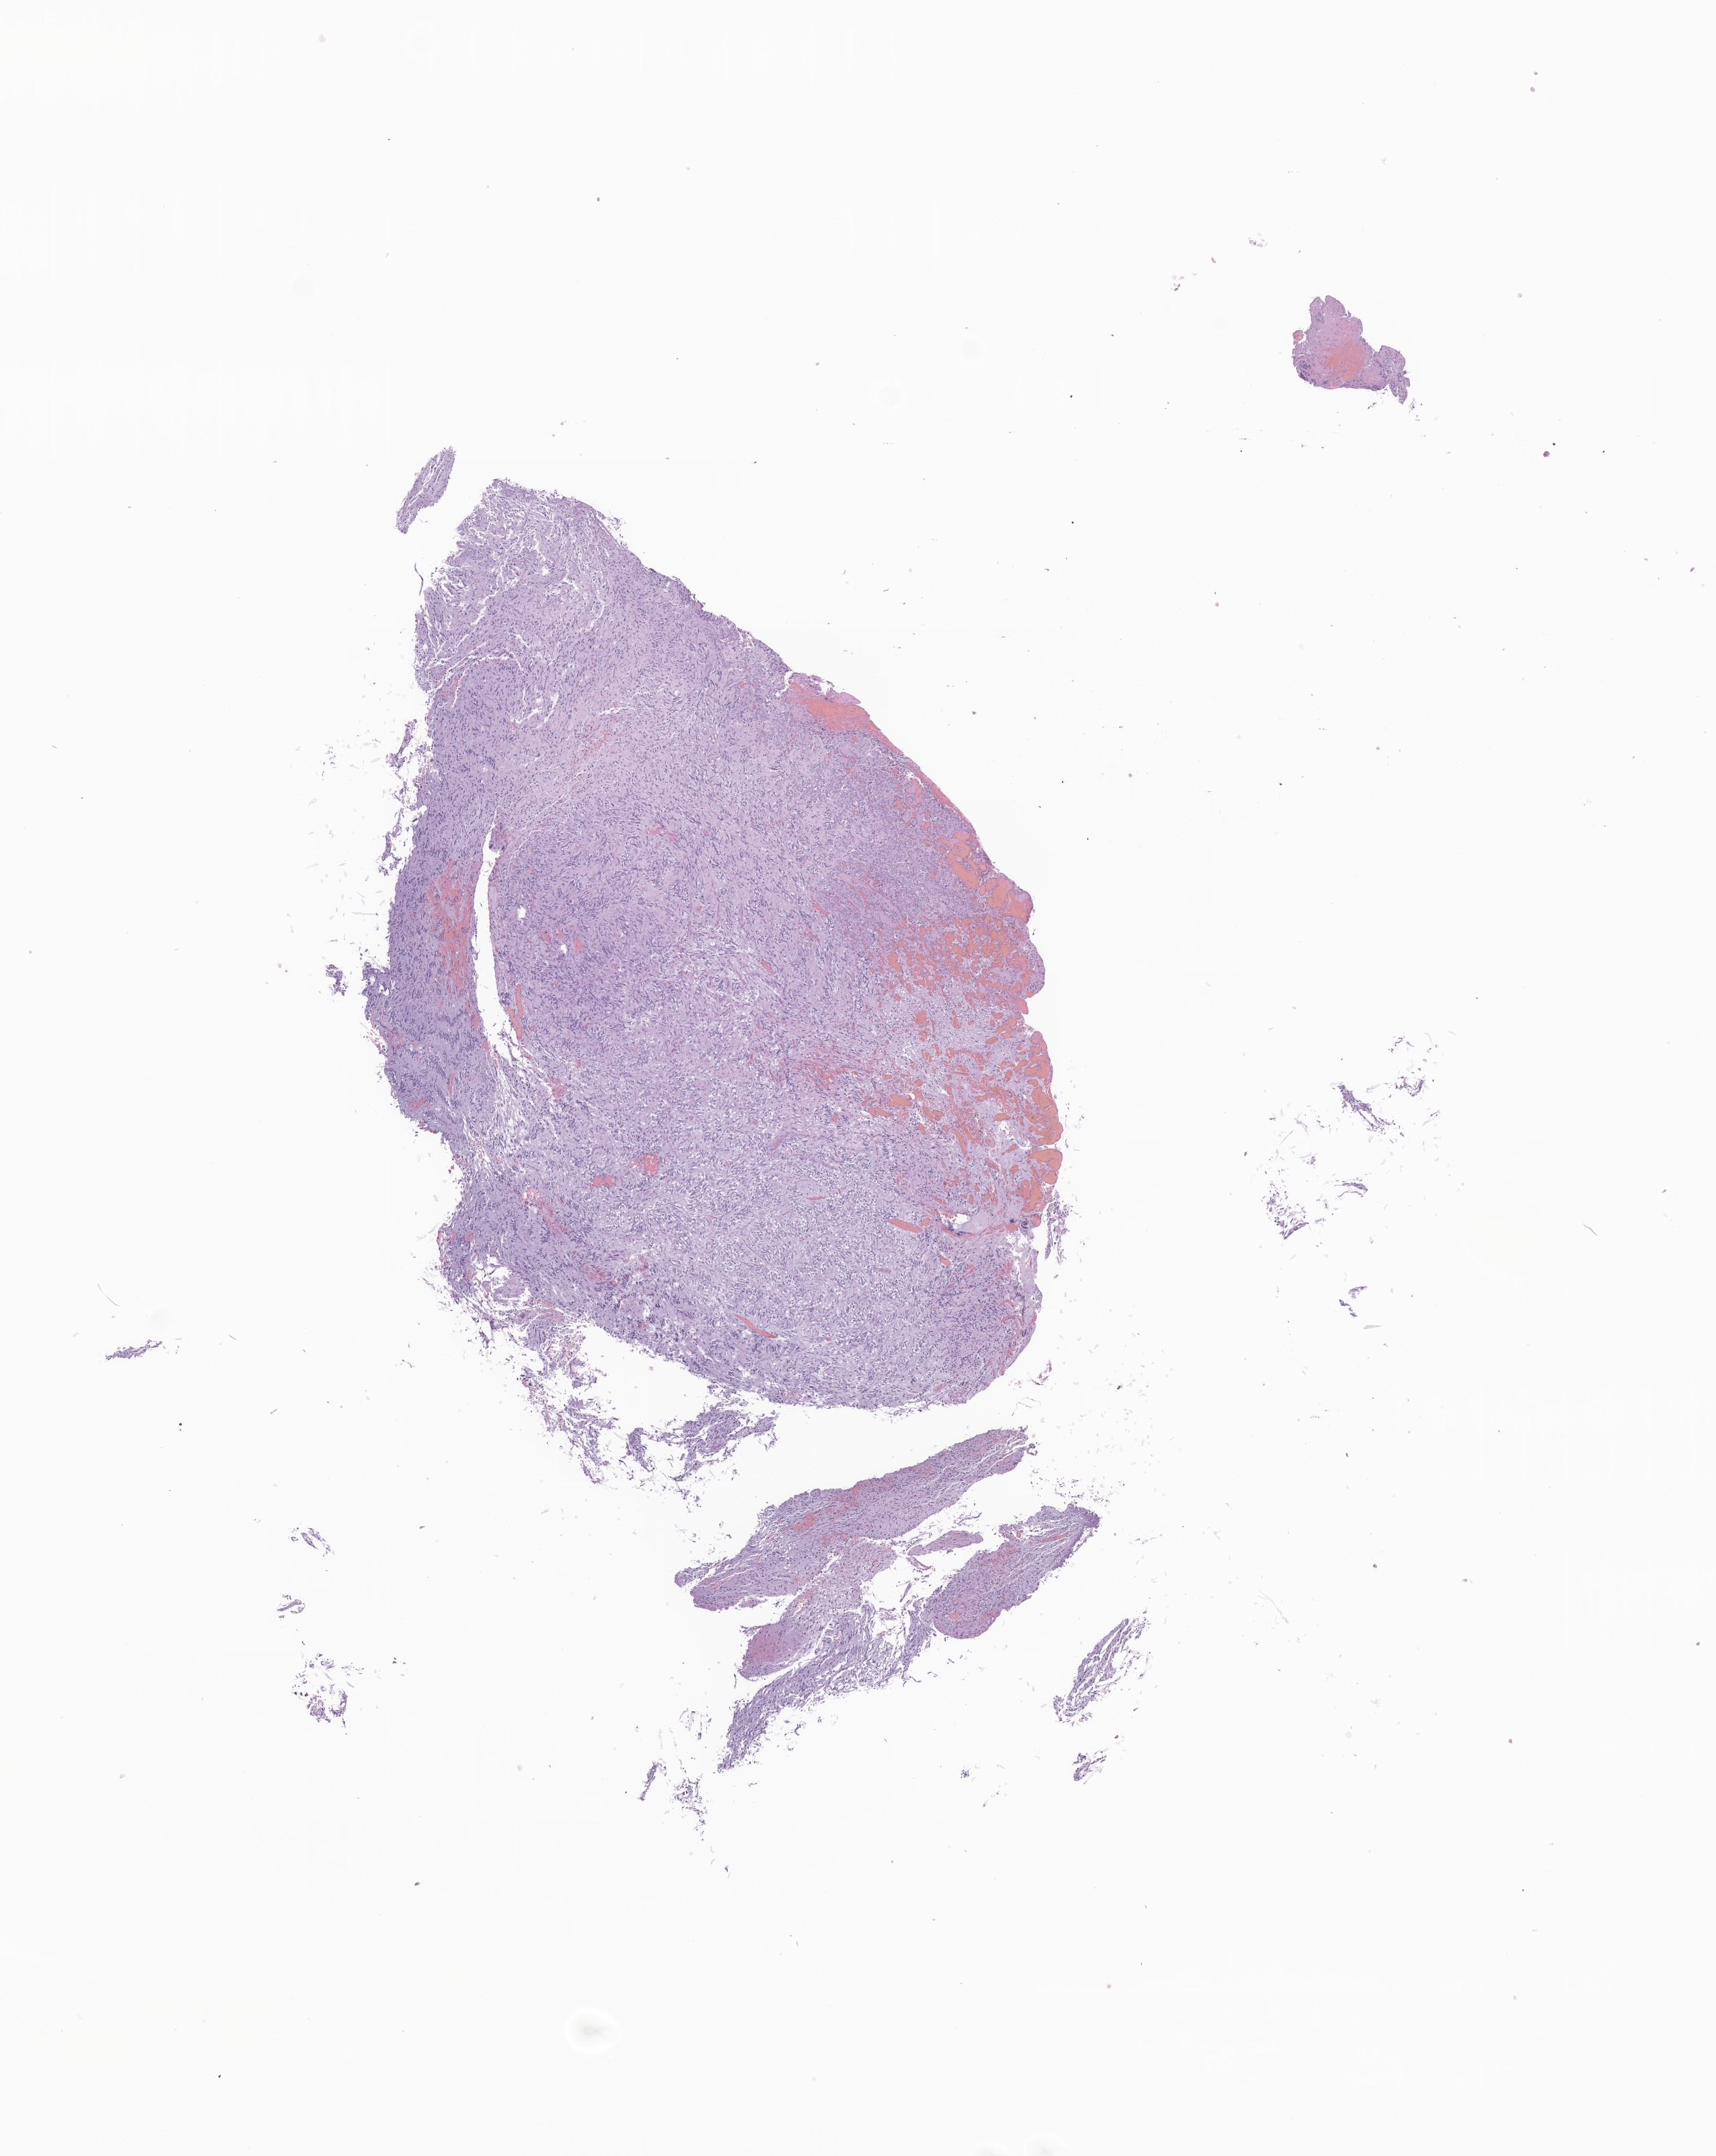
Whole-slide image, haematoxylin and eosin stain of tumor tissue from the cranial and/or facial bone — a low-resolution overview of the entire scanned area, about 10.8 x 13.5 mm, FFPE section. Male patient, age 77 months (6 years 5 months).
Diagnosis: Pilocytic astrocytoma.